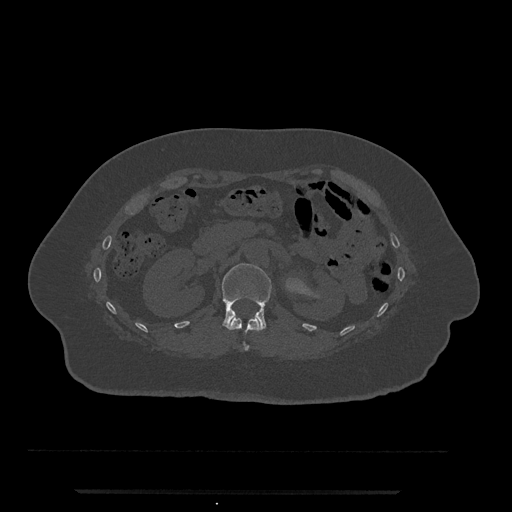
CT including the spine, one axial slice; slice 128 of 797 in the series (ordered by position); bone window (W 1800 / L 400 HU); 512 × 512 image matrix, field of view 440 × 440 mm. Patient: female, 51 years. Case-level facts recorded for this patient, not image findings: primary cancer: neuro; vertebrae with lytic lesions (as recorded): T8.
Outlined on this slice (semi-automatic segmentation, software-assisted and operator-edited):
- L1 vertebra: bounding box [x1, y1, x2, y2] px = [222, 263, 272, 329]
- T12 vertebra: [227, 317, 263, 351]